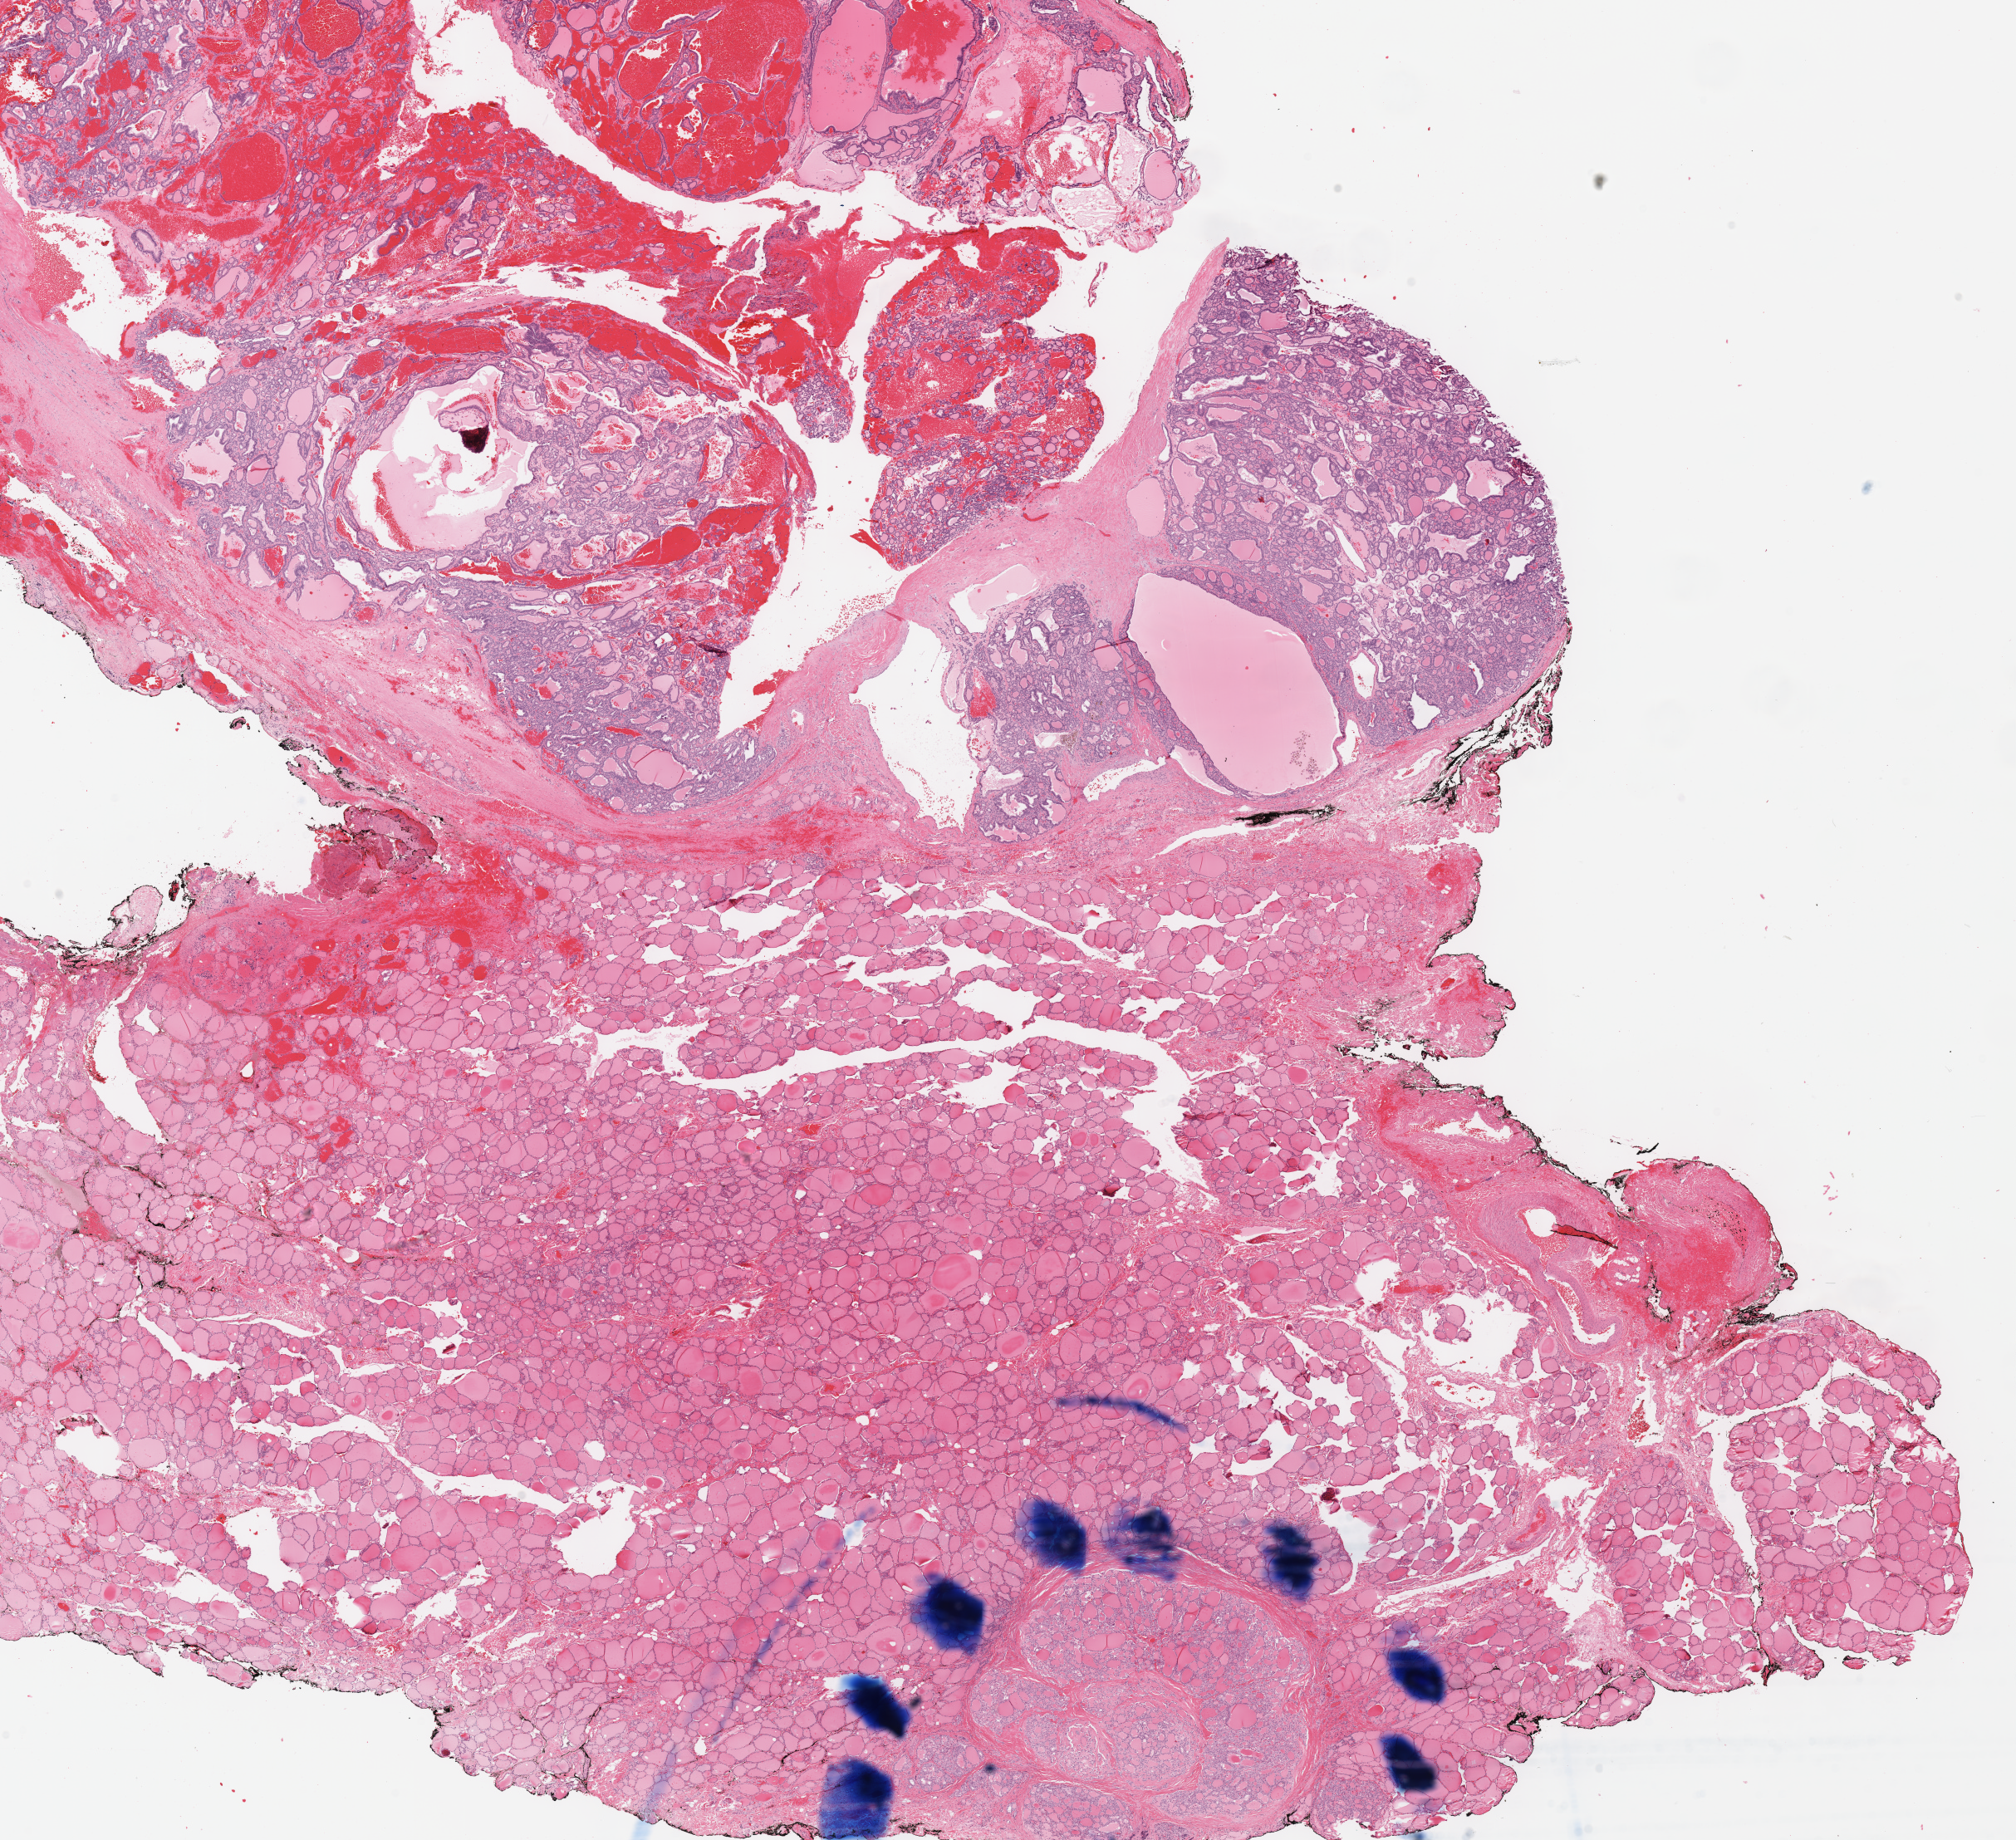
Whole-slide histology image, H&E-stained, whole scanned area (about 19.1 x 17.4 mm, acquisition: 40x scan) shown as a low-resolution overview. FFPE section. Thyroid, primary tumour sample. Female, age 52 years at initial diagnosis.
Pathologic diagnosis: Papillary carcinoma, follicular variant. AJCC pathologic stage: I (7th edition). Laterality: right.